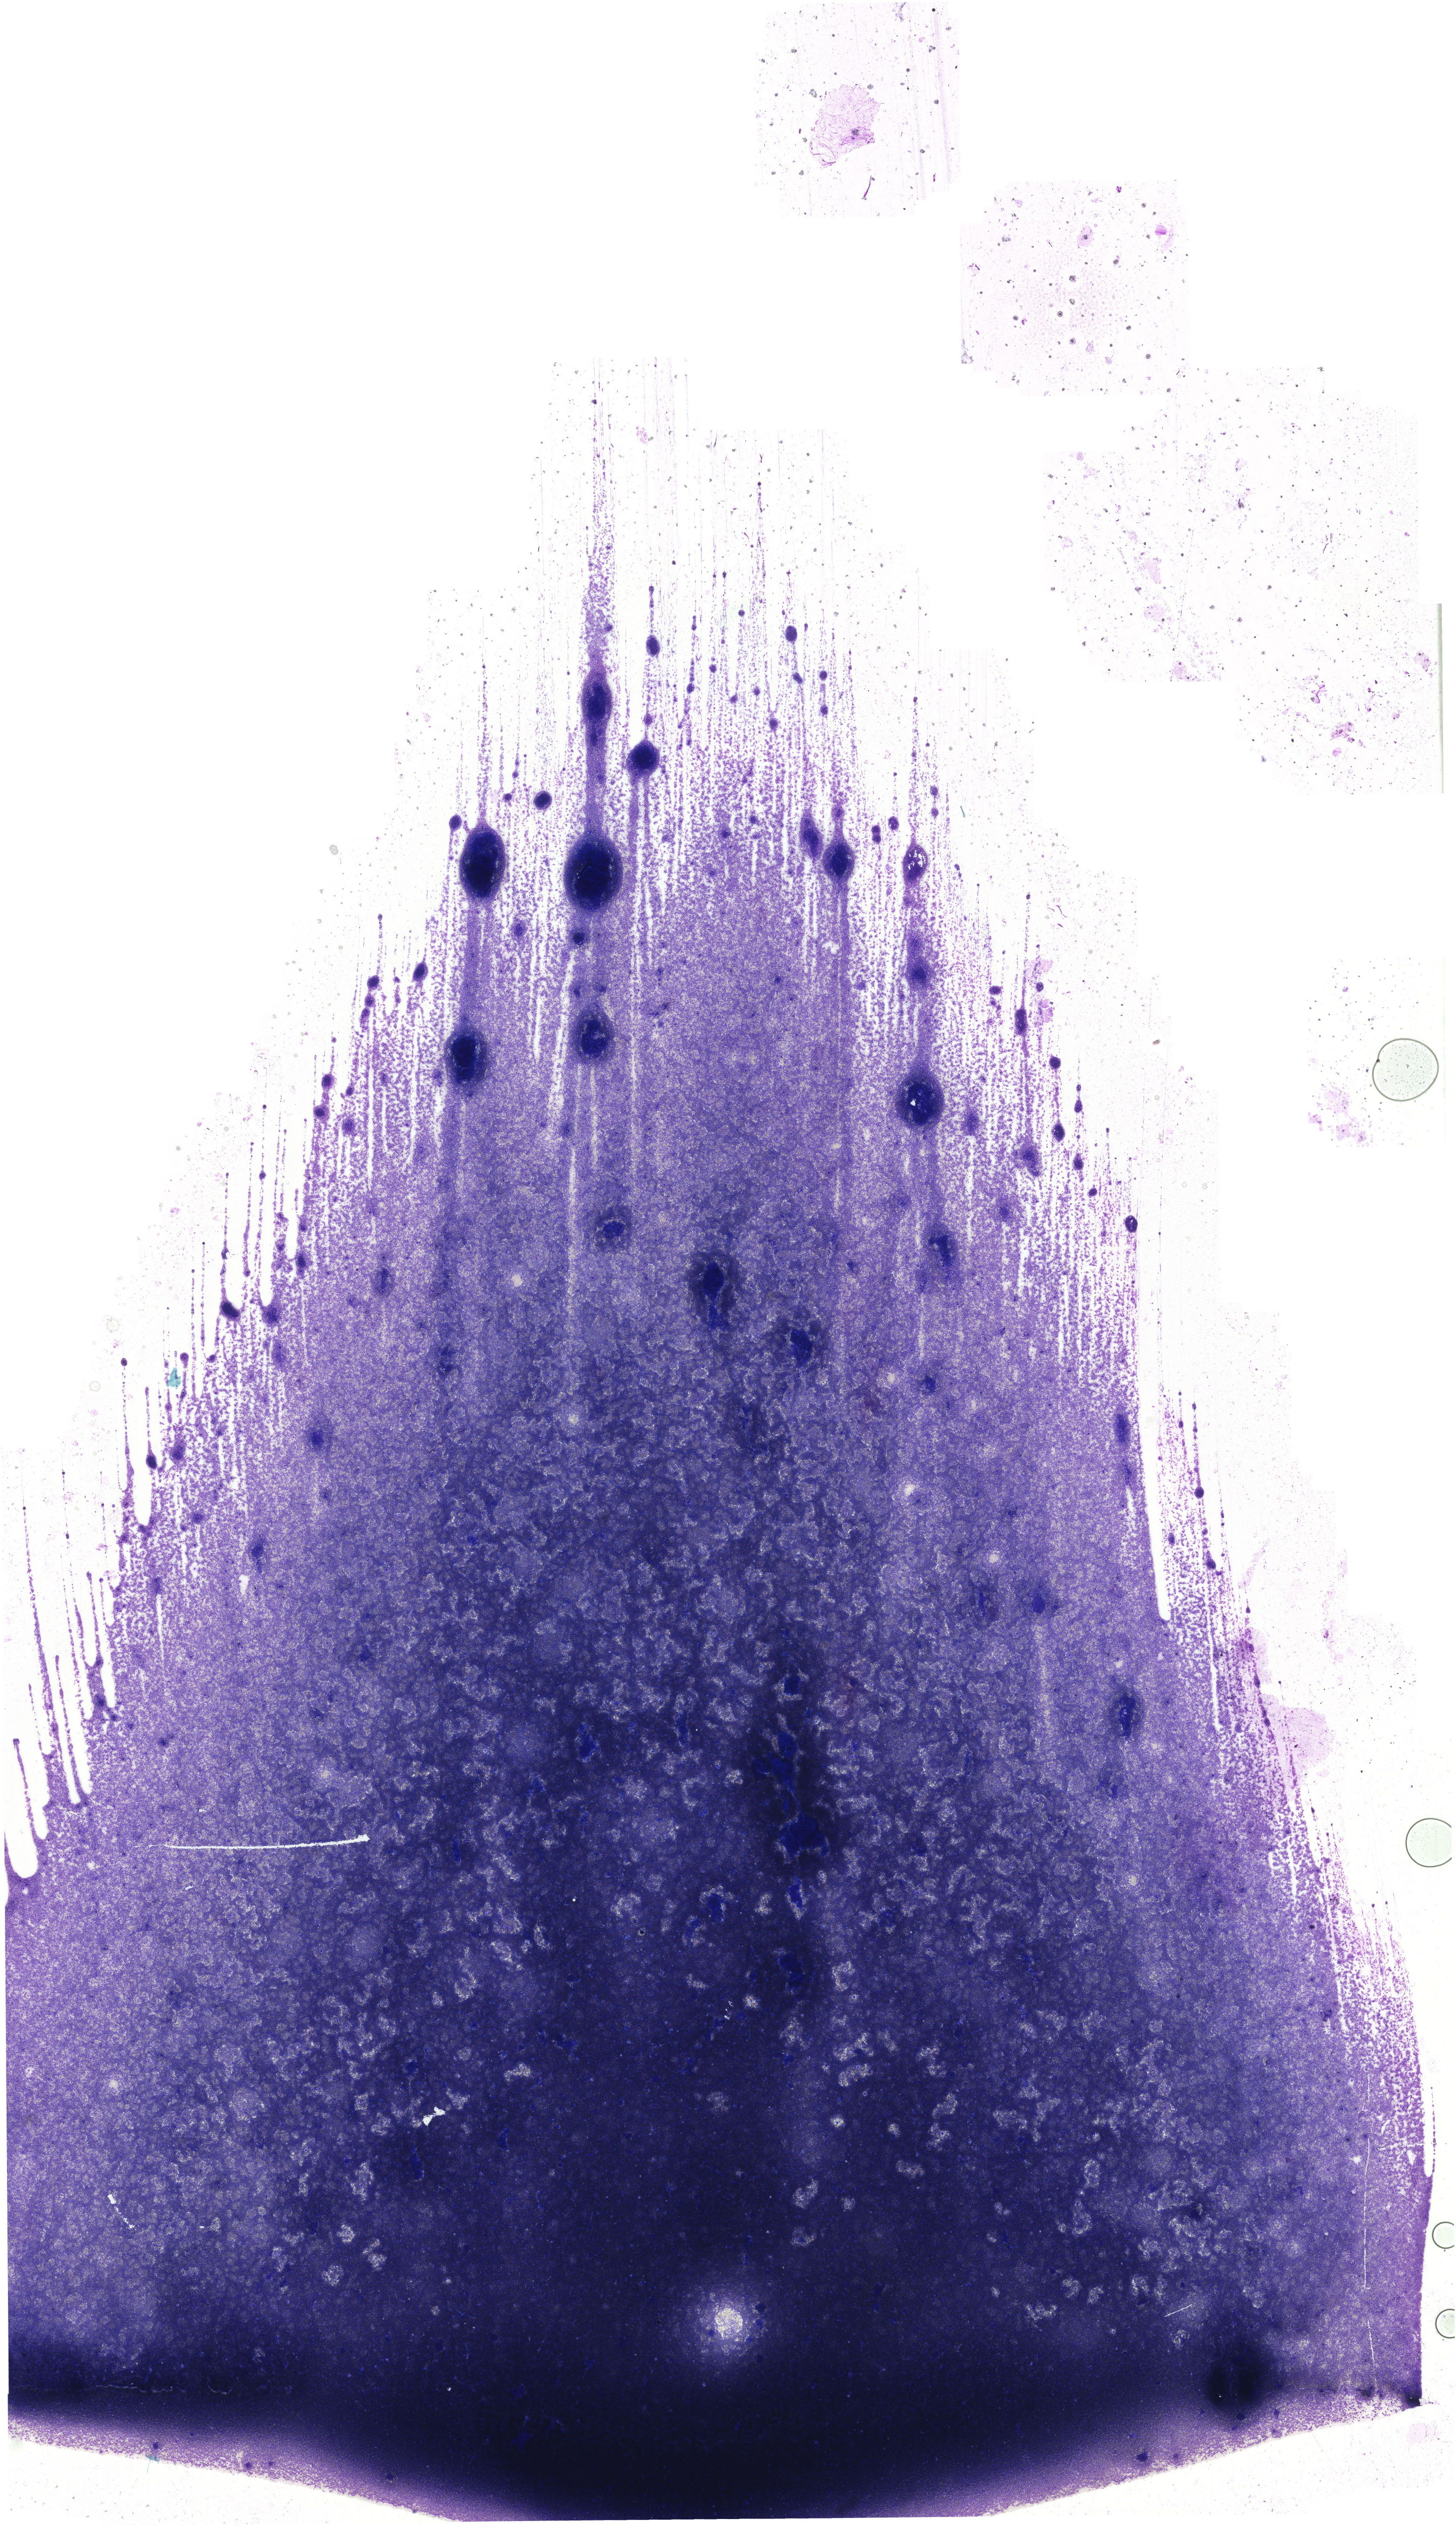
Whole-slide image of a May-Grünwald–Giemsa-stained bone marrow aspirate smear, whole scanned area (about 20.6 x 35.8 mm) shown as a low-resolution overview. Patient sex: female.
* diagnosis: Chronic Phase Chronic Myeloid Leukemia, BCR-ABL1 Positive